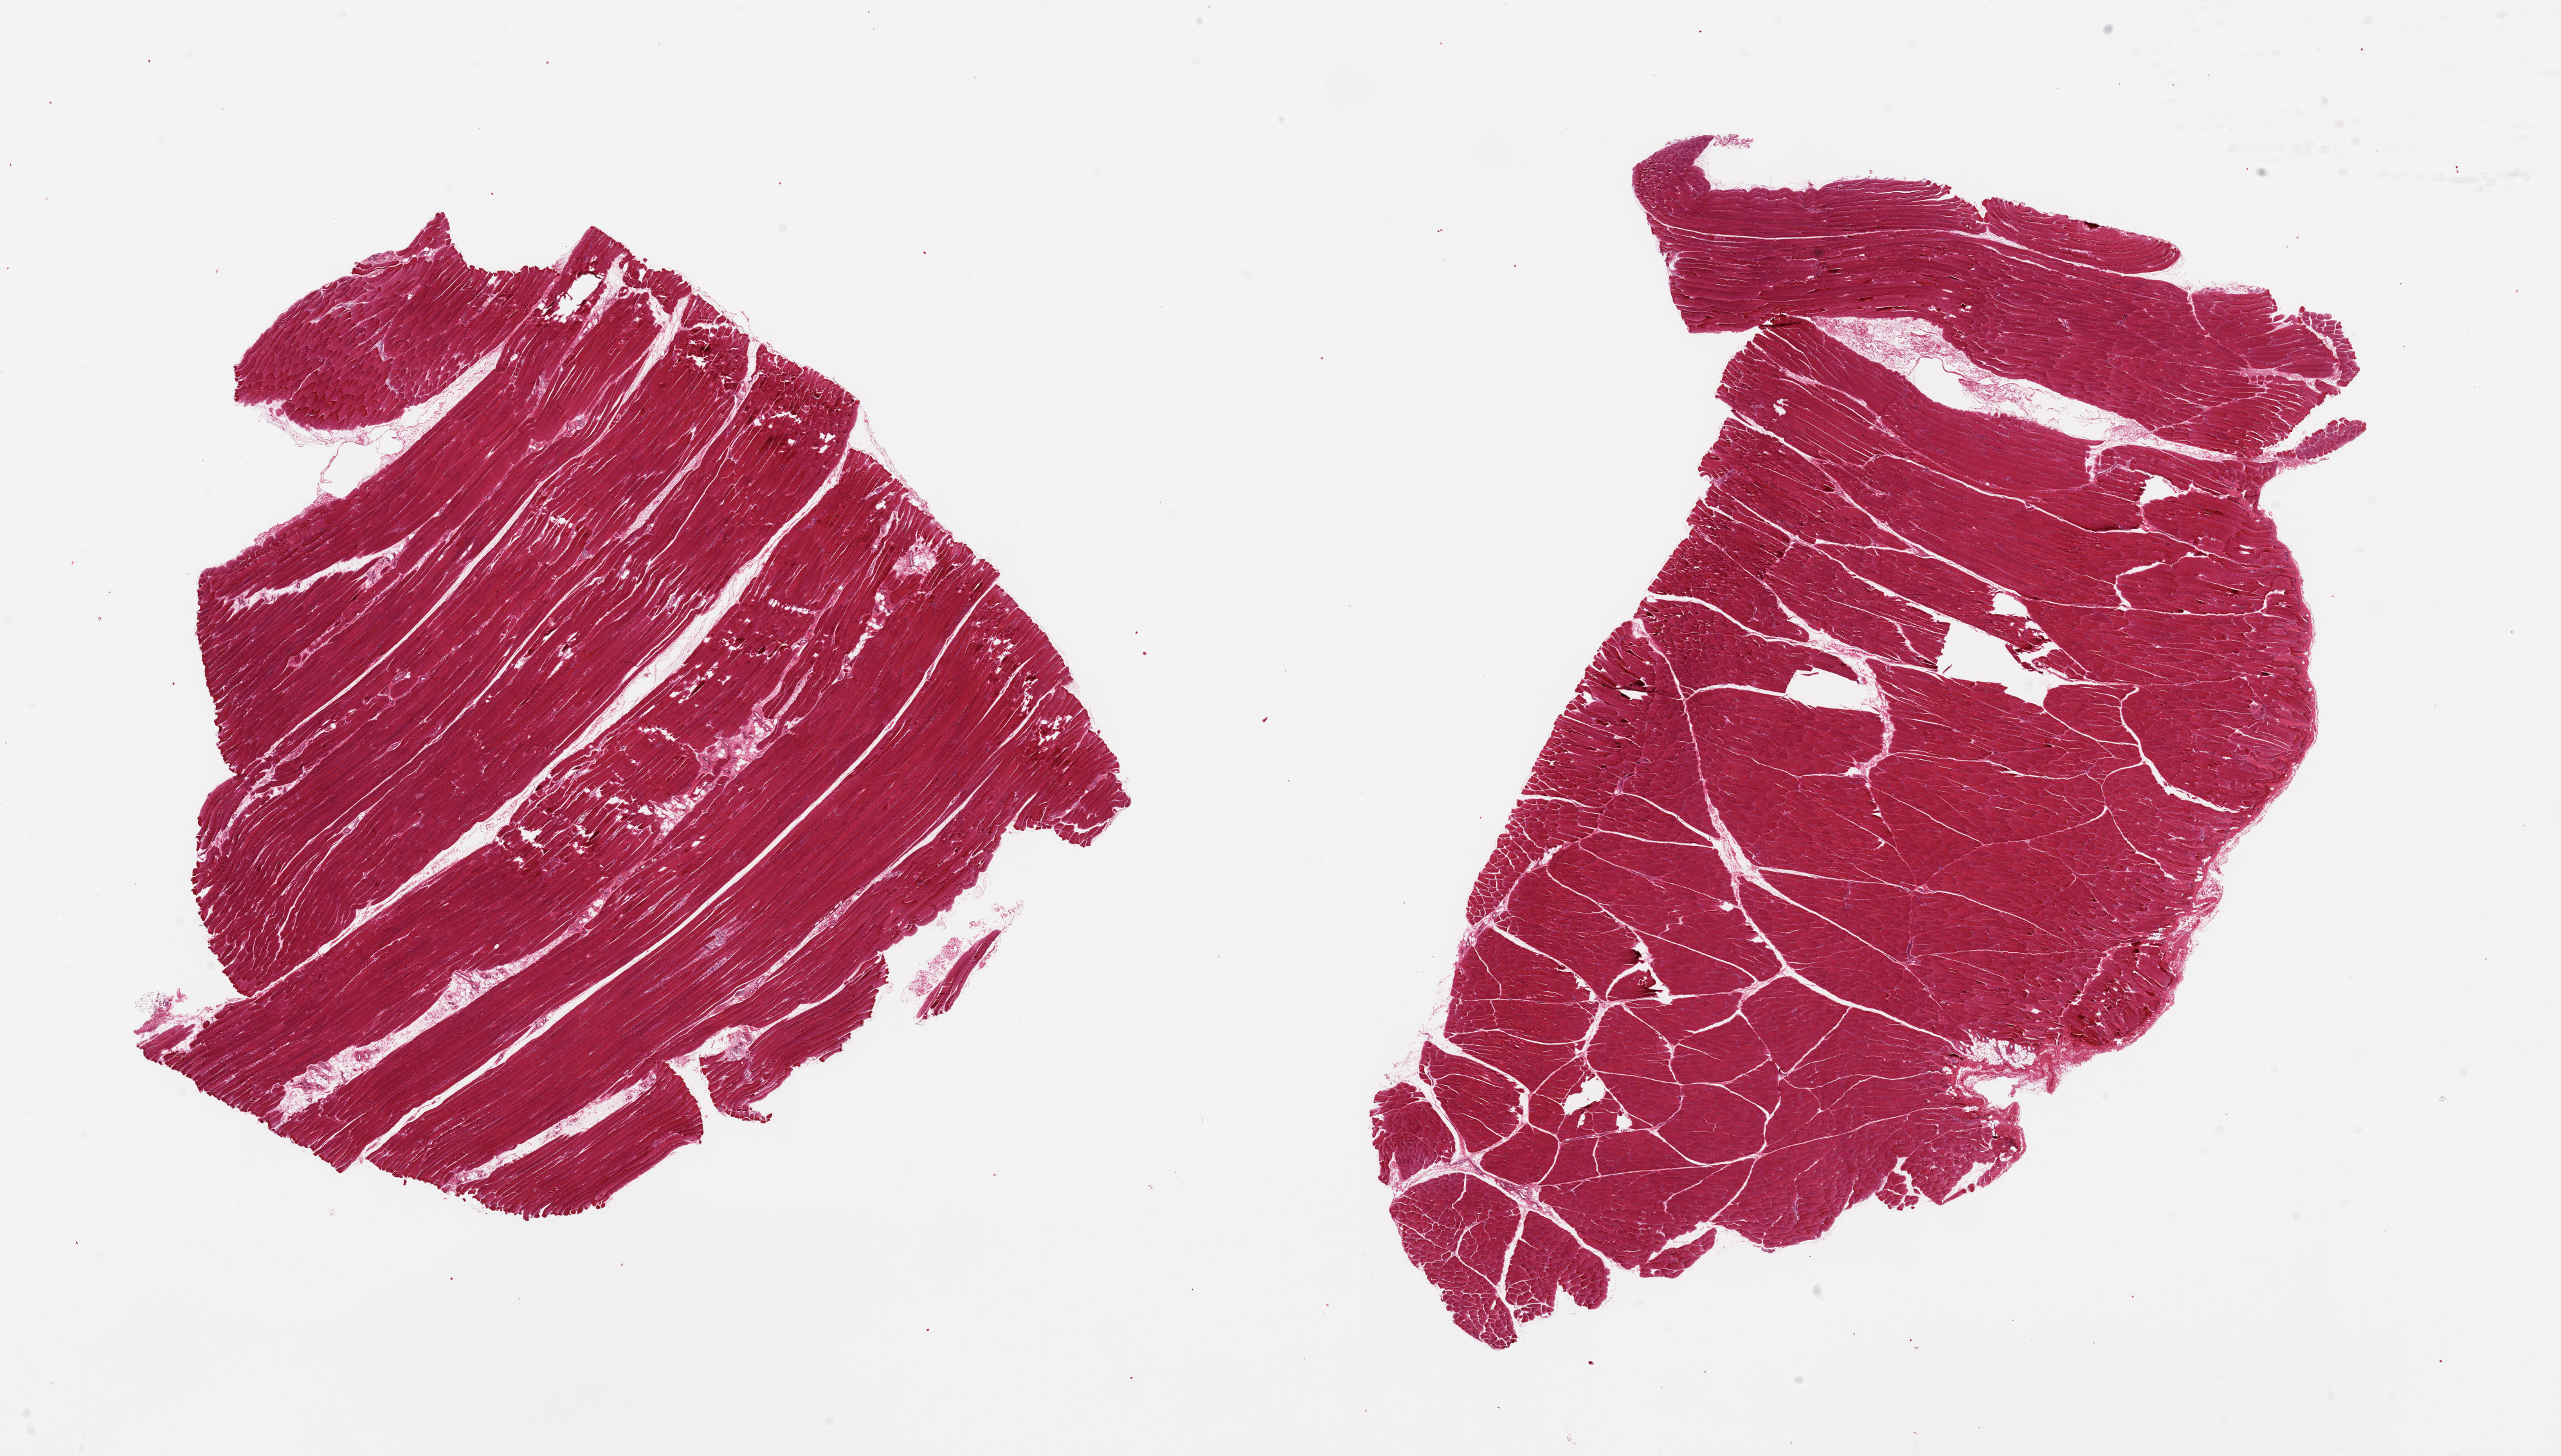
Digitized haematoxylin and eosin-stained section, whole scanned area (about 31.5 x 17.9 mm, slide scanned at 20x) shown as a low-resolution overview; PAXgene-fixed paraffin-embedded (PFPE) section; section of skeletal muscle (target tissue); donor tissue sample.
• review note (as recorded): 2 pieces, 12x12 & 16x11mm